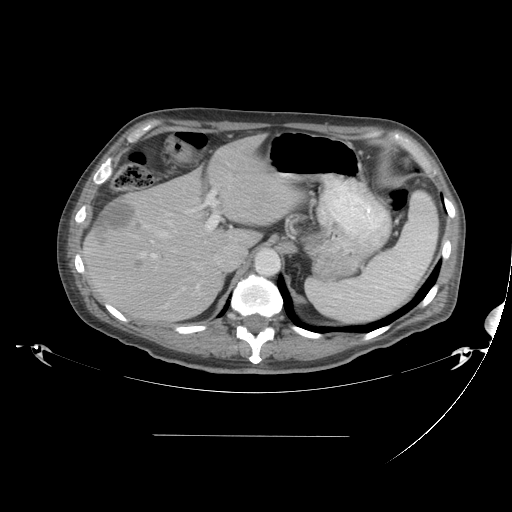
Contrast-enhanced abdominal CT, one axial slice. Position 30 of 48 along the scan axis. Reconstruction kernel STANDARD. Intravenous contrast given. Soft-tissue window (W 400 / L 40 HU). 5 mm slice thickness. 512 × 512 image matrix. Male patient, age 65 years. Case-level facts recorded for this patient, not image findings: diagnosis: colorectal cancer liver metastases, imaged before liver resection; multiple liver metastases: yes.
Outlined on this slice (outlined manually by an expert reader):
- hepatic veins: box from (x=131, y=212) to (x=186, y=291) px
- liver: (x=84, y=137)–(x=298, y=321)
- planned liver remnant (the part of the liver to remain after resection): (x=163, y=138)–(x=297, y=248)
- portal vein (with intrahepatic branches): (x=141, y=176)–(x=232, y=259)
- liver metastasis: (x=133, y=259)–(x=142, y=269)
- liver metastasis: (x=92, y=201)–(x=136, y=239)